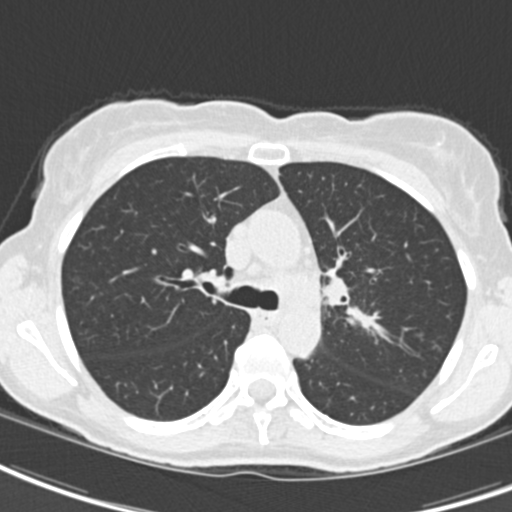
Low-dose screening chest CT, one axial slice. Slice 134 of 189 in the series (ordered by position). Reconstruction kernel B30f. 120 kVp. Lung window (W 1500 / L -600 HU). 2 mm slice thickness. 512 × 512 image matrix, field of view 279 × 279 mm.
Outlined on this slice (outlined manually by an expert reader):
- lesion 2 (tumor, hilum of left lung): box from (x=326, y=278) to (x=349, y=305) px